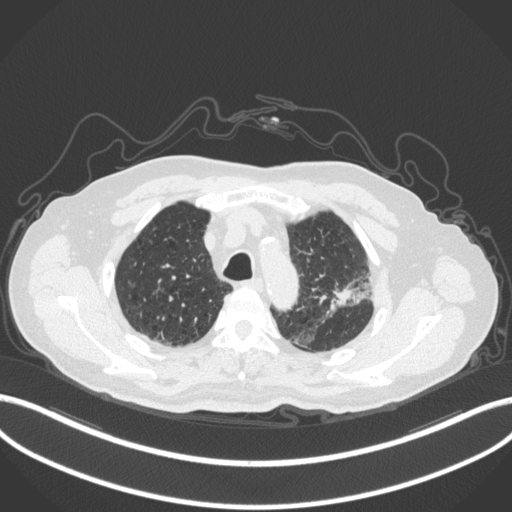
Chest CT, one axial slice; slice 240 of 331 in the series (ordered by position); reconstruction kernel B31f; lung window (W 1500 / L -600 HU); 512 × 512 image matrix, field of view 400 × 400 mm. Male patient, age 79 years. Case-level facts recorded for this patient, not image findings: clinical TNM (as recorded): T2a N1 M1; histopathological grade: G3.
Annotated regions visible in this slice (bounding box drawn by a radiologist):
- lung tumour (recorded histology: adenocarcinoma): bounding box <320,270,371,317> (left, top, right, bottom; pixels)